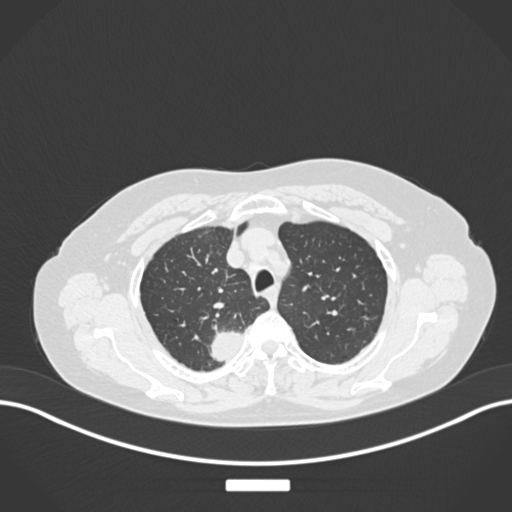
Chest CT, one axial slice; slice 208 of 237 in the series (ordered by position); reconstruction kernel B30f; lung window (W 1500 / L -600 HU); 512 × 512 image matrix, field of view 400 × 400 mm. Patient: female, 62 years. From the clinical record (not read from this slice): clinical TNM (as recorded): T1c N1 M0.
Outlined on this slice (bounding box drawn by a radiologist):
- lung tumour (recorded histology: squamous cell carcinoma): bounding box [x1, y1, x2, y2] px = [205, 325, 248, 364]